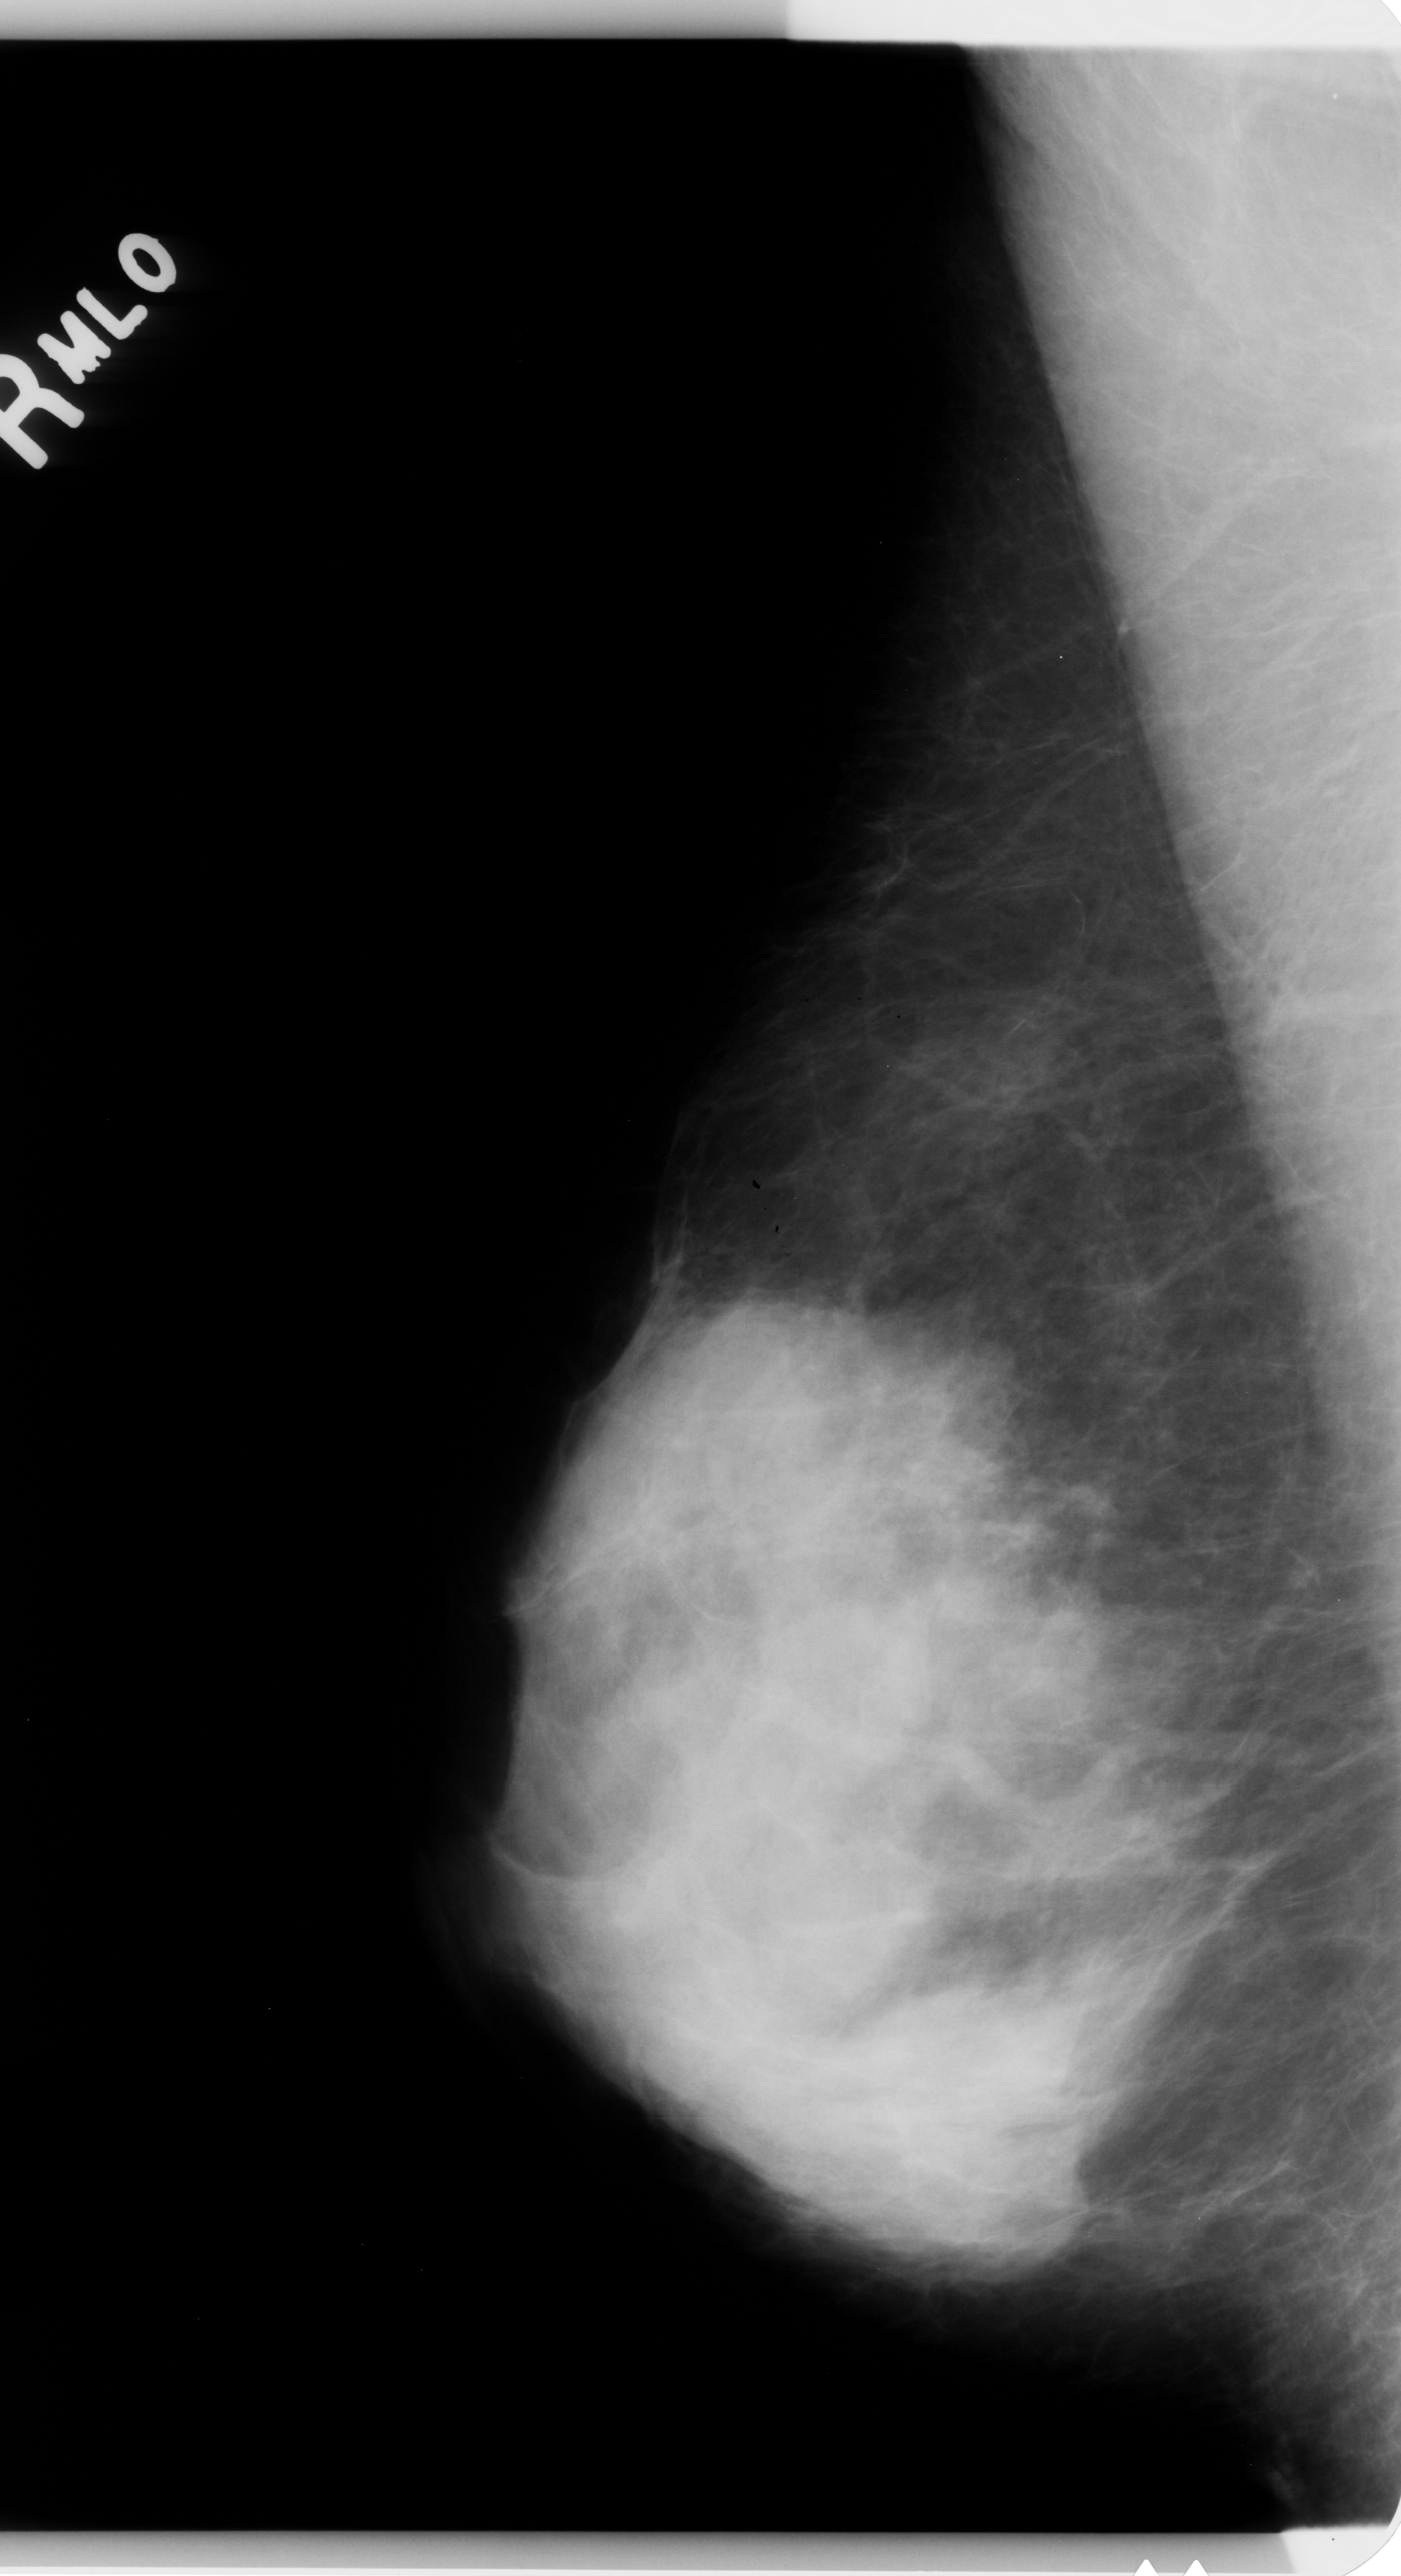
Digitized screen-film mammogram, right breast, mediolateral oblique (MLO) view, BI-RADS breast density category 3 (scale 1–4).
- Finding: mass, shape oval, margins obscured; BI-RADS assessment category 3; pathology (as recorded): benign.